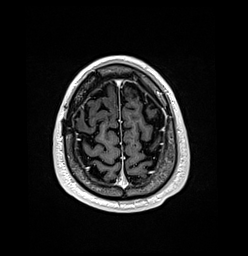
Brain MRI from a brain-tumour surgery series, one axial slice; slice 27 of 176 in the series (ordered by position); T1-weighted post-contrast; 1 mm slice thickness; 248 × 256 image matrix. Case-level facts recorded for this patient, not image findings: histopathology: Oligodendroglioma; WHO grade: 3; IDH mutation: yes; tumour location: Right Frontal.
Outlined on this slice (outlined manually by an expert reader):
- previous resection cavity: bounding box (x1, y1, x2, y2) in pixels: (73, 109, 81, 120)